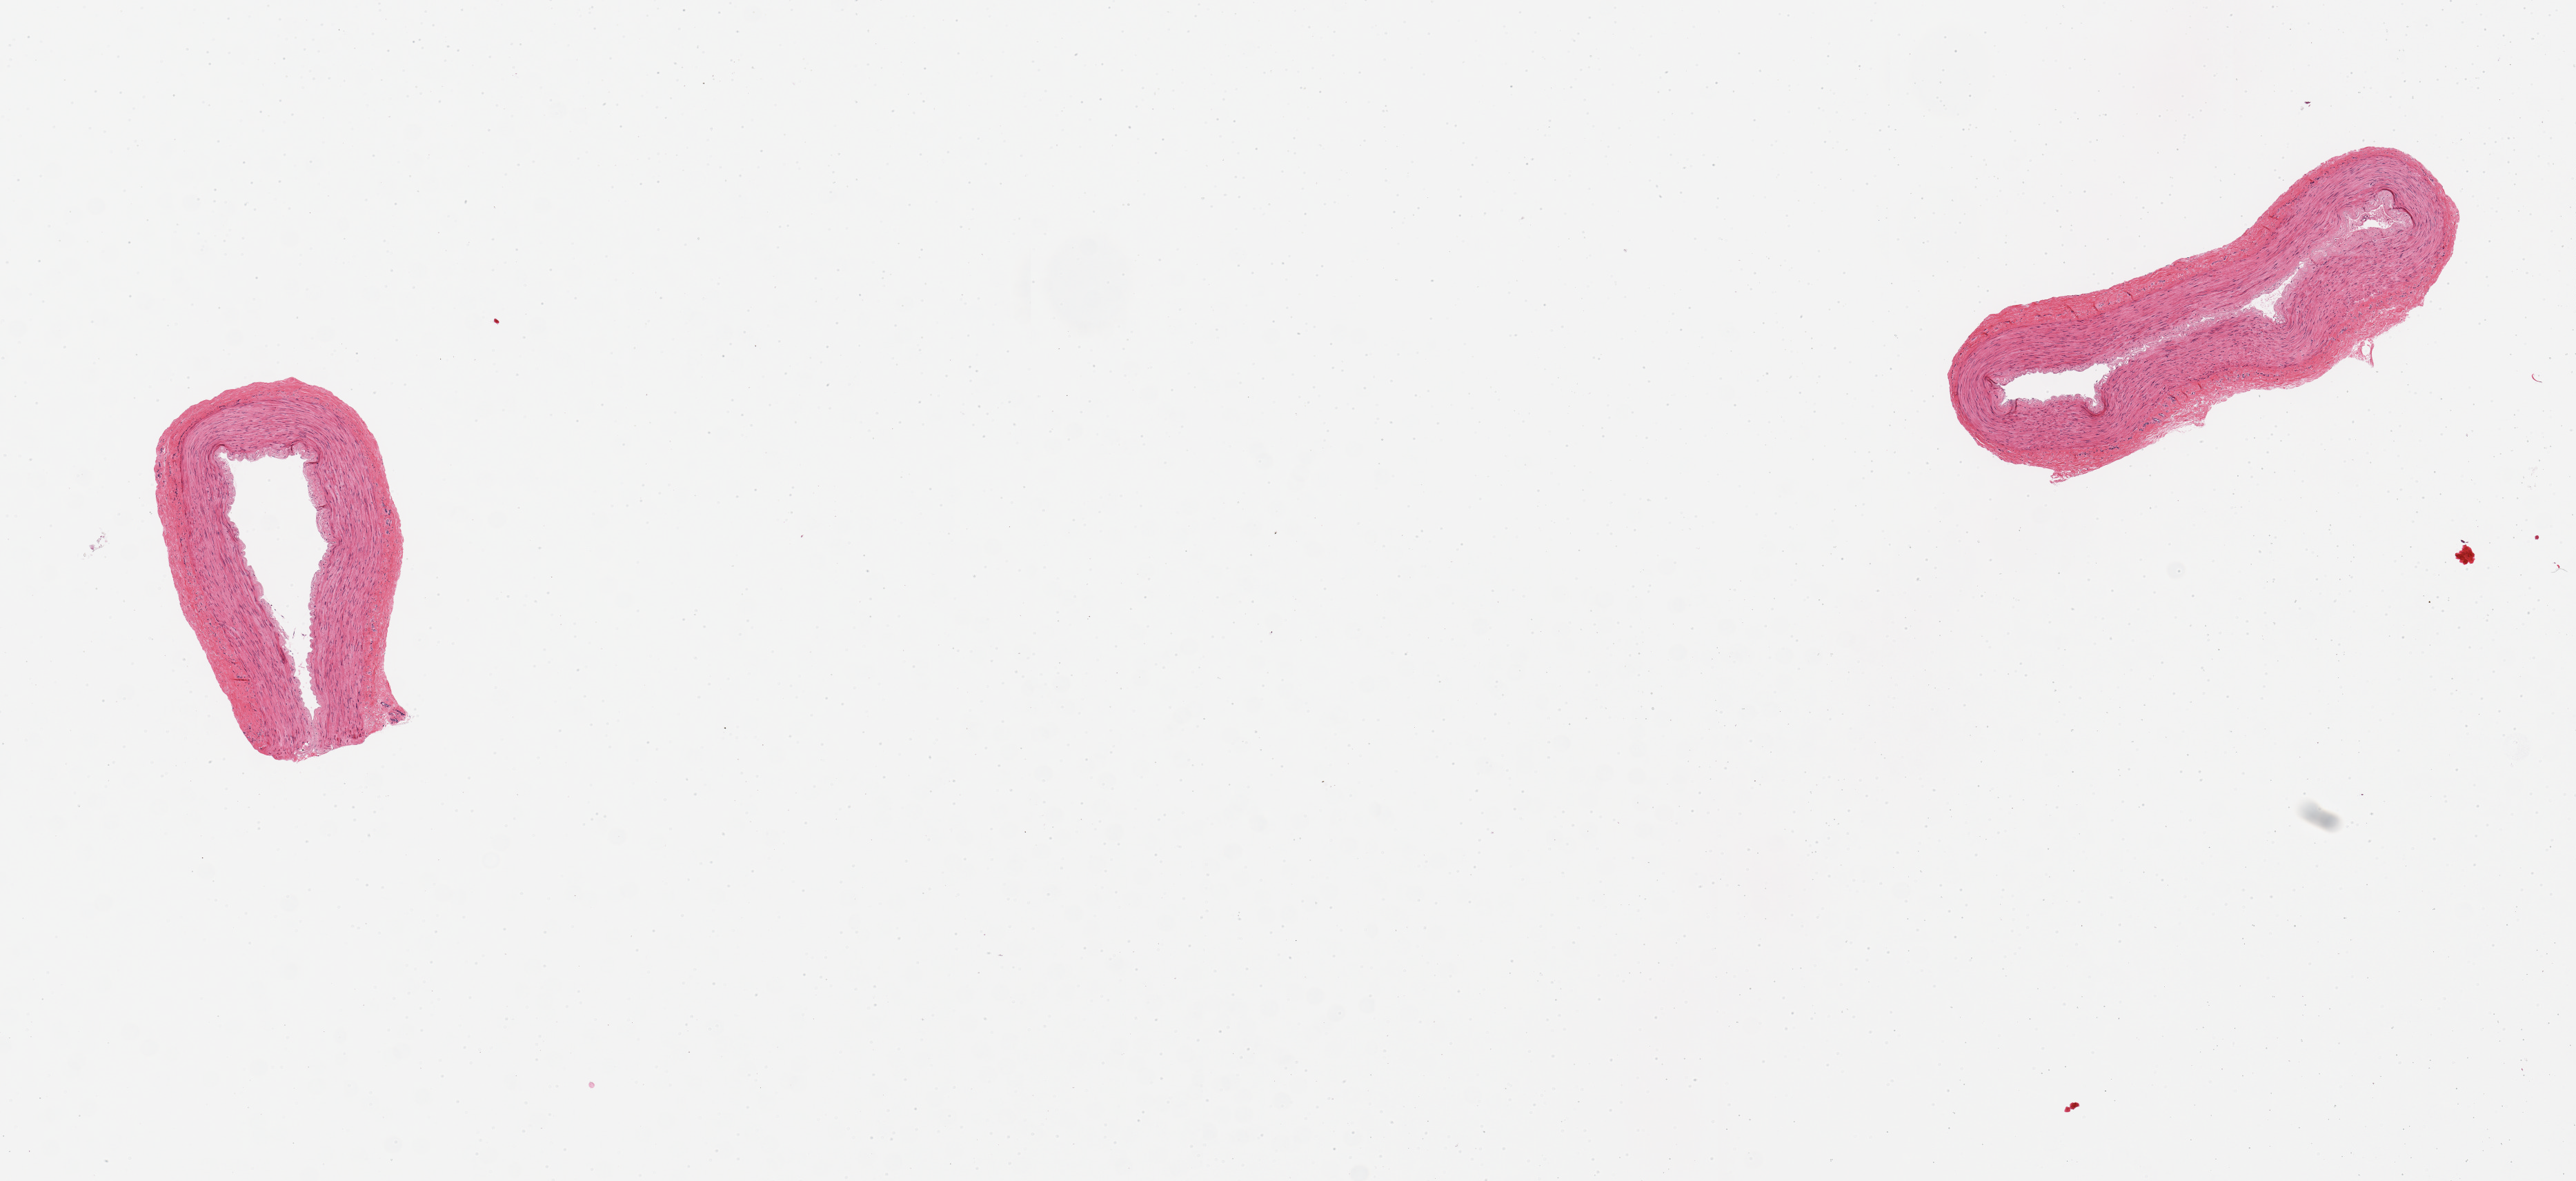
Whole-slide image, haematoxylin and eosin stain, low-resolution overview of the scanned area, about 14.8 x 6.8 mm. PAXgene-fixed paraffin-embedded (PFPE) section. Section of tibial artery (target tissue). Tissue donor sample. Donor sex: male.
* pathologist's review note for this sample: 2 pieces, good clean specimens, minimal fat